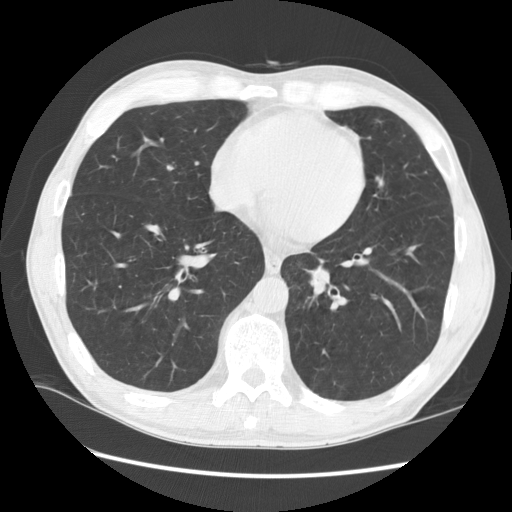
Low-dose screening chest CT, one axial slice. Reconstruction kernel STANDARD. 120 kVp. Lung window (W 1500 / L -600 HU). 2.5 mm slice thickness. 512 × 512 image matrix, field of view 360 × 360 mm.
Structures marked on this image (manually delineated by an expert):
- lesion 2 (nodule, lower lobe of left lung): bounding box [x1, y1, x2, y2] px = [310, 275, 327, 294]